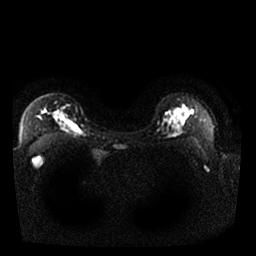
Breast MRI, one axial slice. Slice 21 of 25 in the series (ordered by position). Diffusion-weighted series; image 2 of 4 stored at this slice position (different b-values; order by instance number). 1.5 T. 256 × 256 image matrix, field of view 340 × 340 mm. Female patient.
Annotated regions visible in this slice (manually delineated by an expert):
- tumour on diffusion-weighted imaging: box from (x=55, y=111) to (x=63, y=119) px